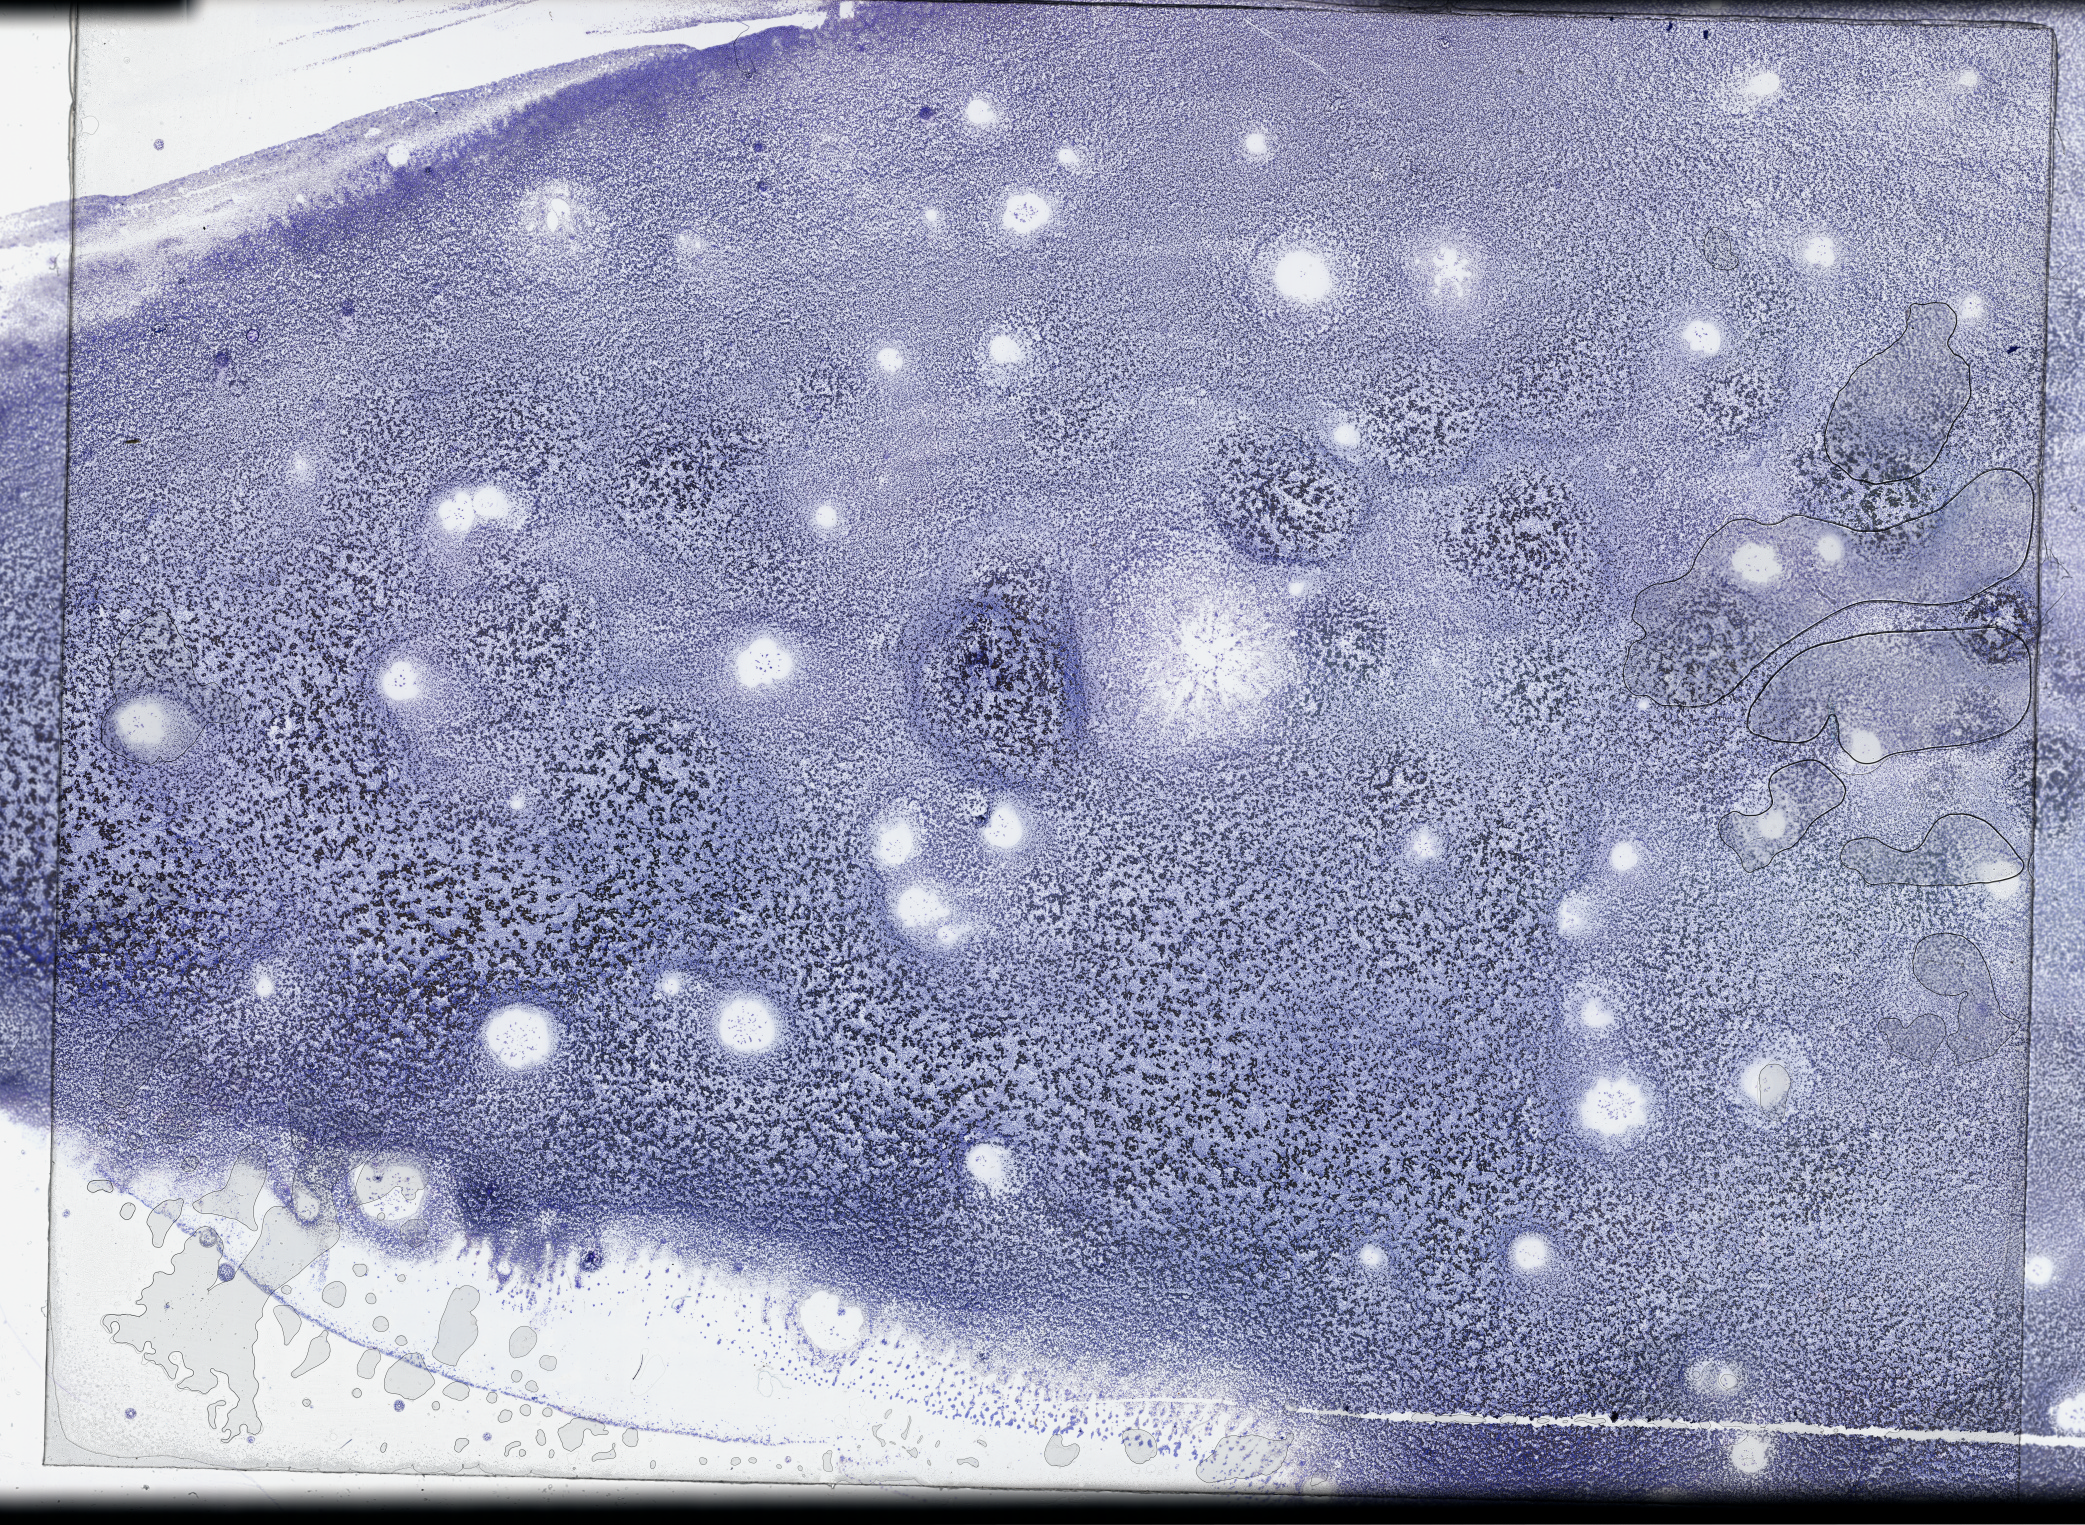
Digitized Hematoxylin and eosin (H&E) stained tissue section (whole slide), low-resolution overview of the scanned area, about 33.7 x 24.6 mm, bone marrow (leukaemic) sample. Male, 47 y/o. Blasts: 70%.
* diagnosis: Acute Myeloid Leukemia
* FAB classification: M4